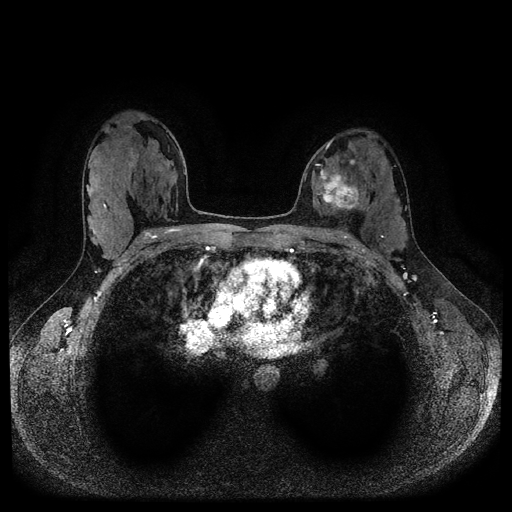
Breast MRI (dynamic contrast-enhanced, multi-phase), one axial slice. Slice 61 of 116 in the series (ordered by position). Dynamic contrast-enhanced series, time point 2 of 5 at this slice position (early post-contrast). 1.5 T. TE 2.6 ms, TR 5.3 ms. 2 mm slice thickness. 512 × 512 image matrix, field of view 350 × 350 mm. Patient: female, 33 years.
Annotated regions visible in this slice (semi-automatically segmented with operator editing):
- breast lesion (labelled 'tumour' in the annotation; benign lesions carry a separate 'benign' label): bounding box (x1, y1, x2, y2) in pixels: (316, 166, 363, 212)